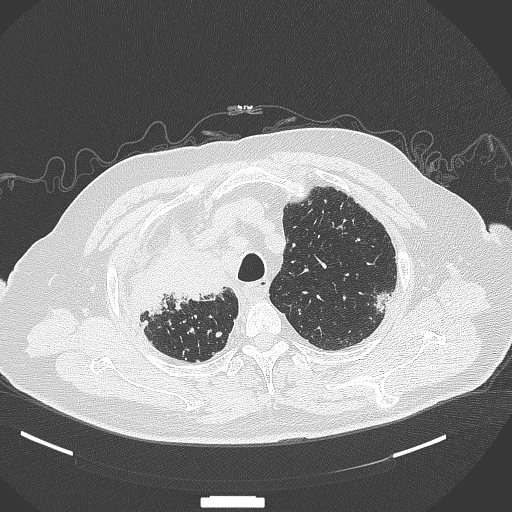
Chest CT, one axial slice. Reconstruction kernel B70f. Lung window (W 1500 / L -600 HU). 1 mm slice thickness. 512 × 512 image matrix. Male patient, age 69 years. From the clinical record (not read from this slice): clinical TNM (as recorded): T4 N3 M1.
Structures marked on this image (bounding box drawn by a radiologist):
- lung tumour (recorded histology: adenocarcinoma): bounding box [x1, y1, x2, y2] px = [134, 243, 233, 316]